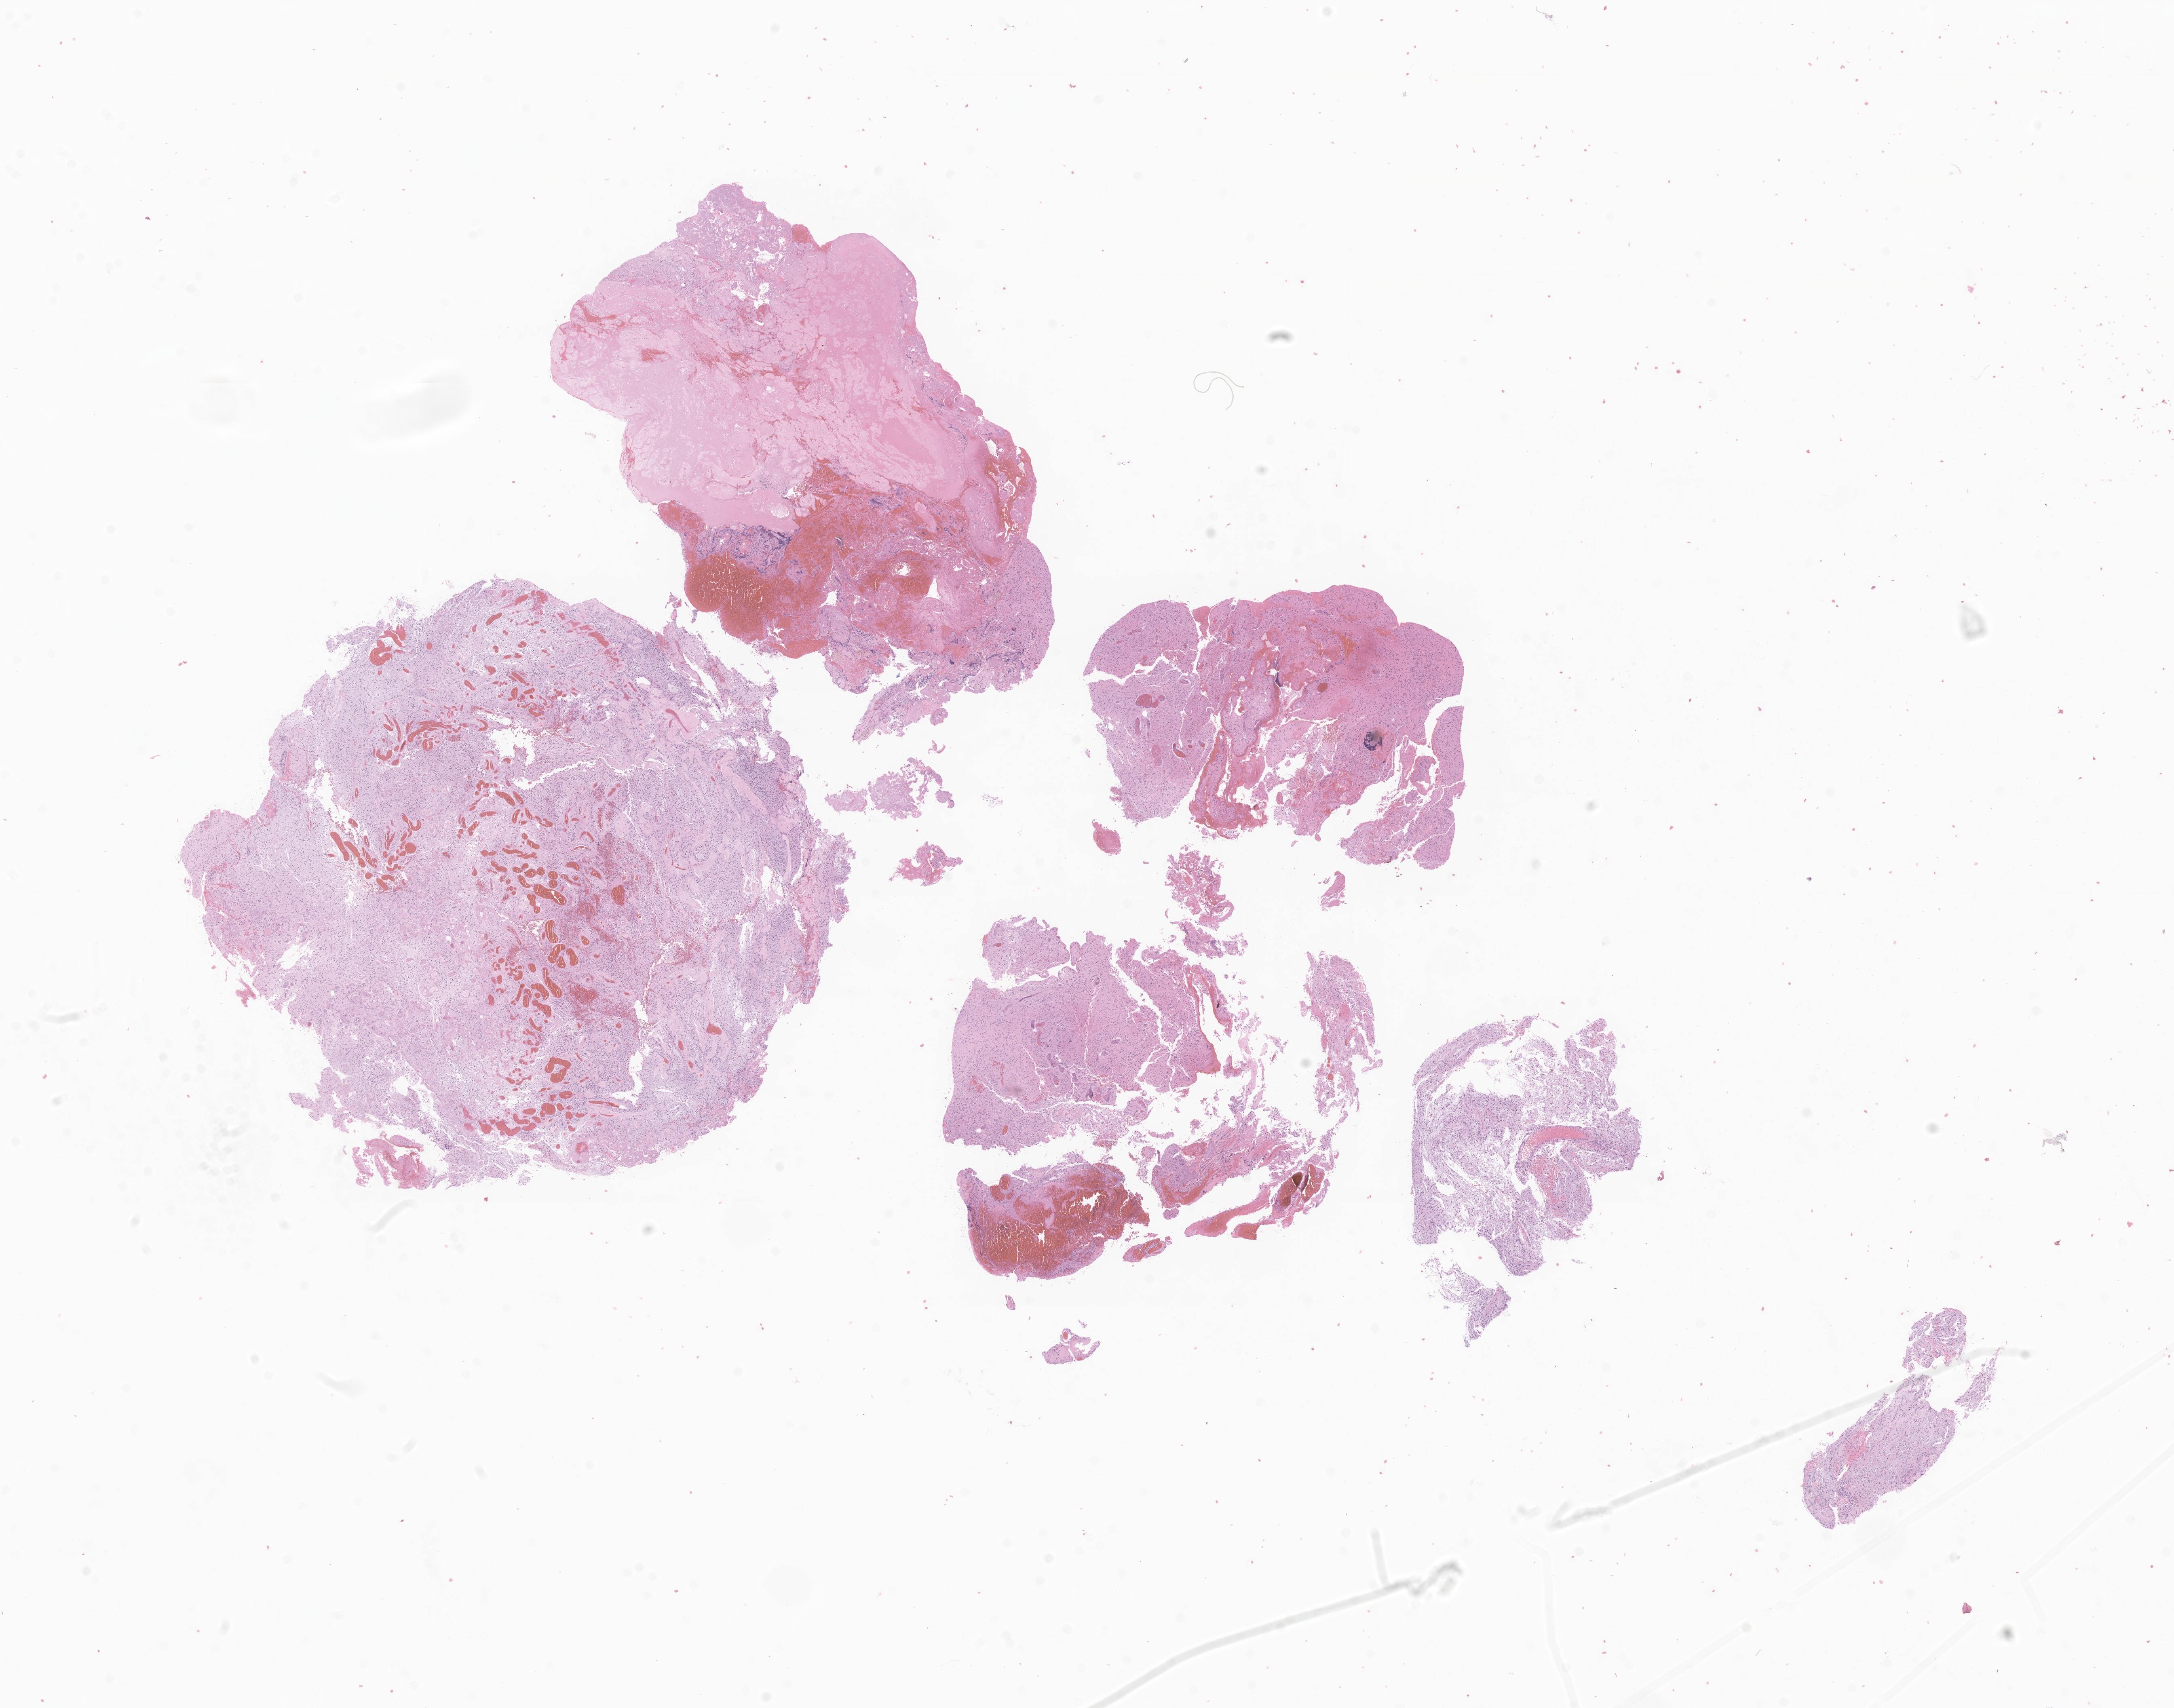
Digitized hematoxylin and eosin (H&E)-stained section of tumor tissue from the cerebellum — whole scanned area (about 22.7 x 17.8 mm) shown as a low-resolution overview, formalin-fixed, paraffin-embedded (FFPE) tissue. Patient male; age 202 months (16 years 10 months).
Diagnosis (ICD-O-3 morphology term): Pilocytic astrocytoma.